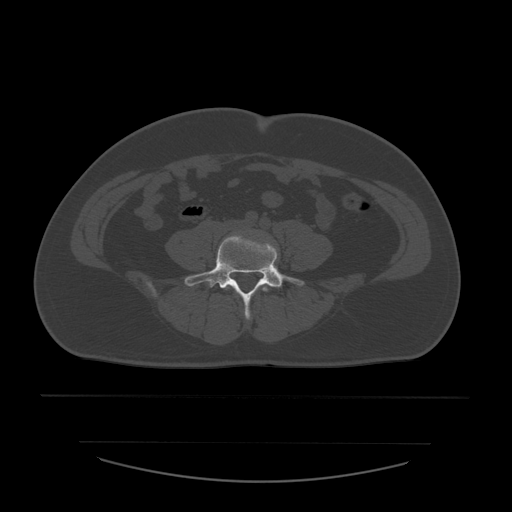
CT including the spine, one axial slice; position 127 of 532 along the scan axis; 120 kVp; bone window (W 1800 / L 400 HU); 1.25 mm slice thickness; 512 × 512 image matrix, field of view 441 × 441 mm. Patient age 44 years. Case-level facts recorded for this patient, not image findings: primary cancer: soft tissue sarcoma.
Outlined on this slice (semi-automatically segmented with operator editing):
- L4 vertebra: bounding box <225,287,269,292> (left, top, right, bottom; pixels)
- L5 vertebra: <184,236,304,319>